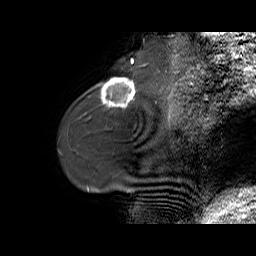
Breast MRI (dynamic contrast-enhanced), one sagittal slice; position 16 of 70 along the scan axis; dynamic contrast-enhanced series, time point 2 of 6 at this slice position (early post-contrast); 1.5 T; TE 5.5 ms, TR 32.9 ms; 4 mm slice thickness; 256 × 256 image matrix, field of view 240 × 240 mm. Female patient. Case-level facts recorded for this patient, not image findings: setting: breast cancer imaged before/during neoadjuvant chemotherapy; receptor status: HER2-positive.
Annotated regions visible in this slice (semi-automatically segmented with operator editing):
- analysis volume of interest (the breast-tissue region the enhancement analysis was run in; not a lesion): bounding box (x1, y1, x2, y2) in pixels: (96, 73, 141, 113)
- tumour enhancement mask (voxels above the 100 % enhancement threshold inside the analysis volume of interest): (101, 78, 135, 106)